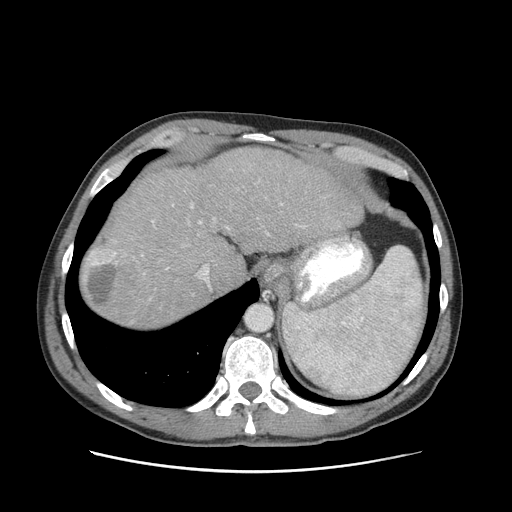
Contrast-enhanced abdominal CT (liver protocol), one axial slice; soft-tissue window (W 400 / L 40 HU); 2.5 mm slice thickness; 512 × 512 image matrix, field of view 380 × 380 mm. From the clinical record (not read from this slice): diagnosis: hepatocellular carcinoma (patient treated with transarterial chemoembolisation; whether this scan precedes or follows treatment is not stated here); TNM stage (as recorded): Stage-II; Child-Pugh class: A; tumour differentiation: moderately differentiated; tumour nodularity: multinodular.
Annotated regions visible in this slice (semi-automatic segmentation, software-assisted and operator-edited):
- abdominal aorta: bounding box (x1, y1, x2, y2) in pixels: (246, 305, 272, 331)
- liver parenchyma outside the tumour (the mass and vessels are separate outlines, so this box may not span the whole liver): (80, 148, 364, 328)
- mass: (86, 247, 145, 319)
- liver vessels: (167, 204, 283, 281)